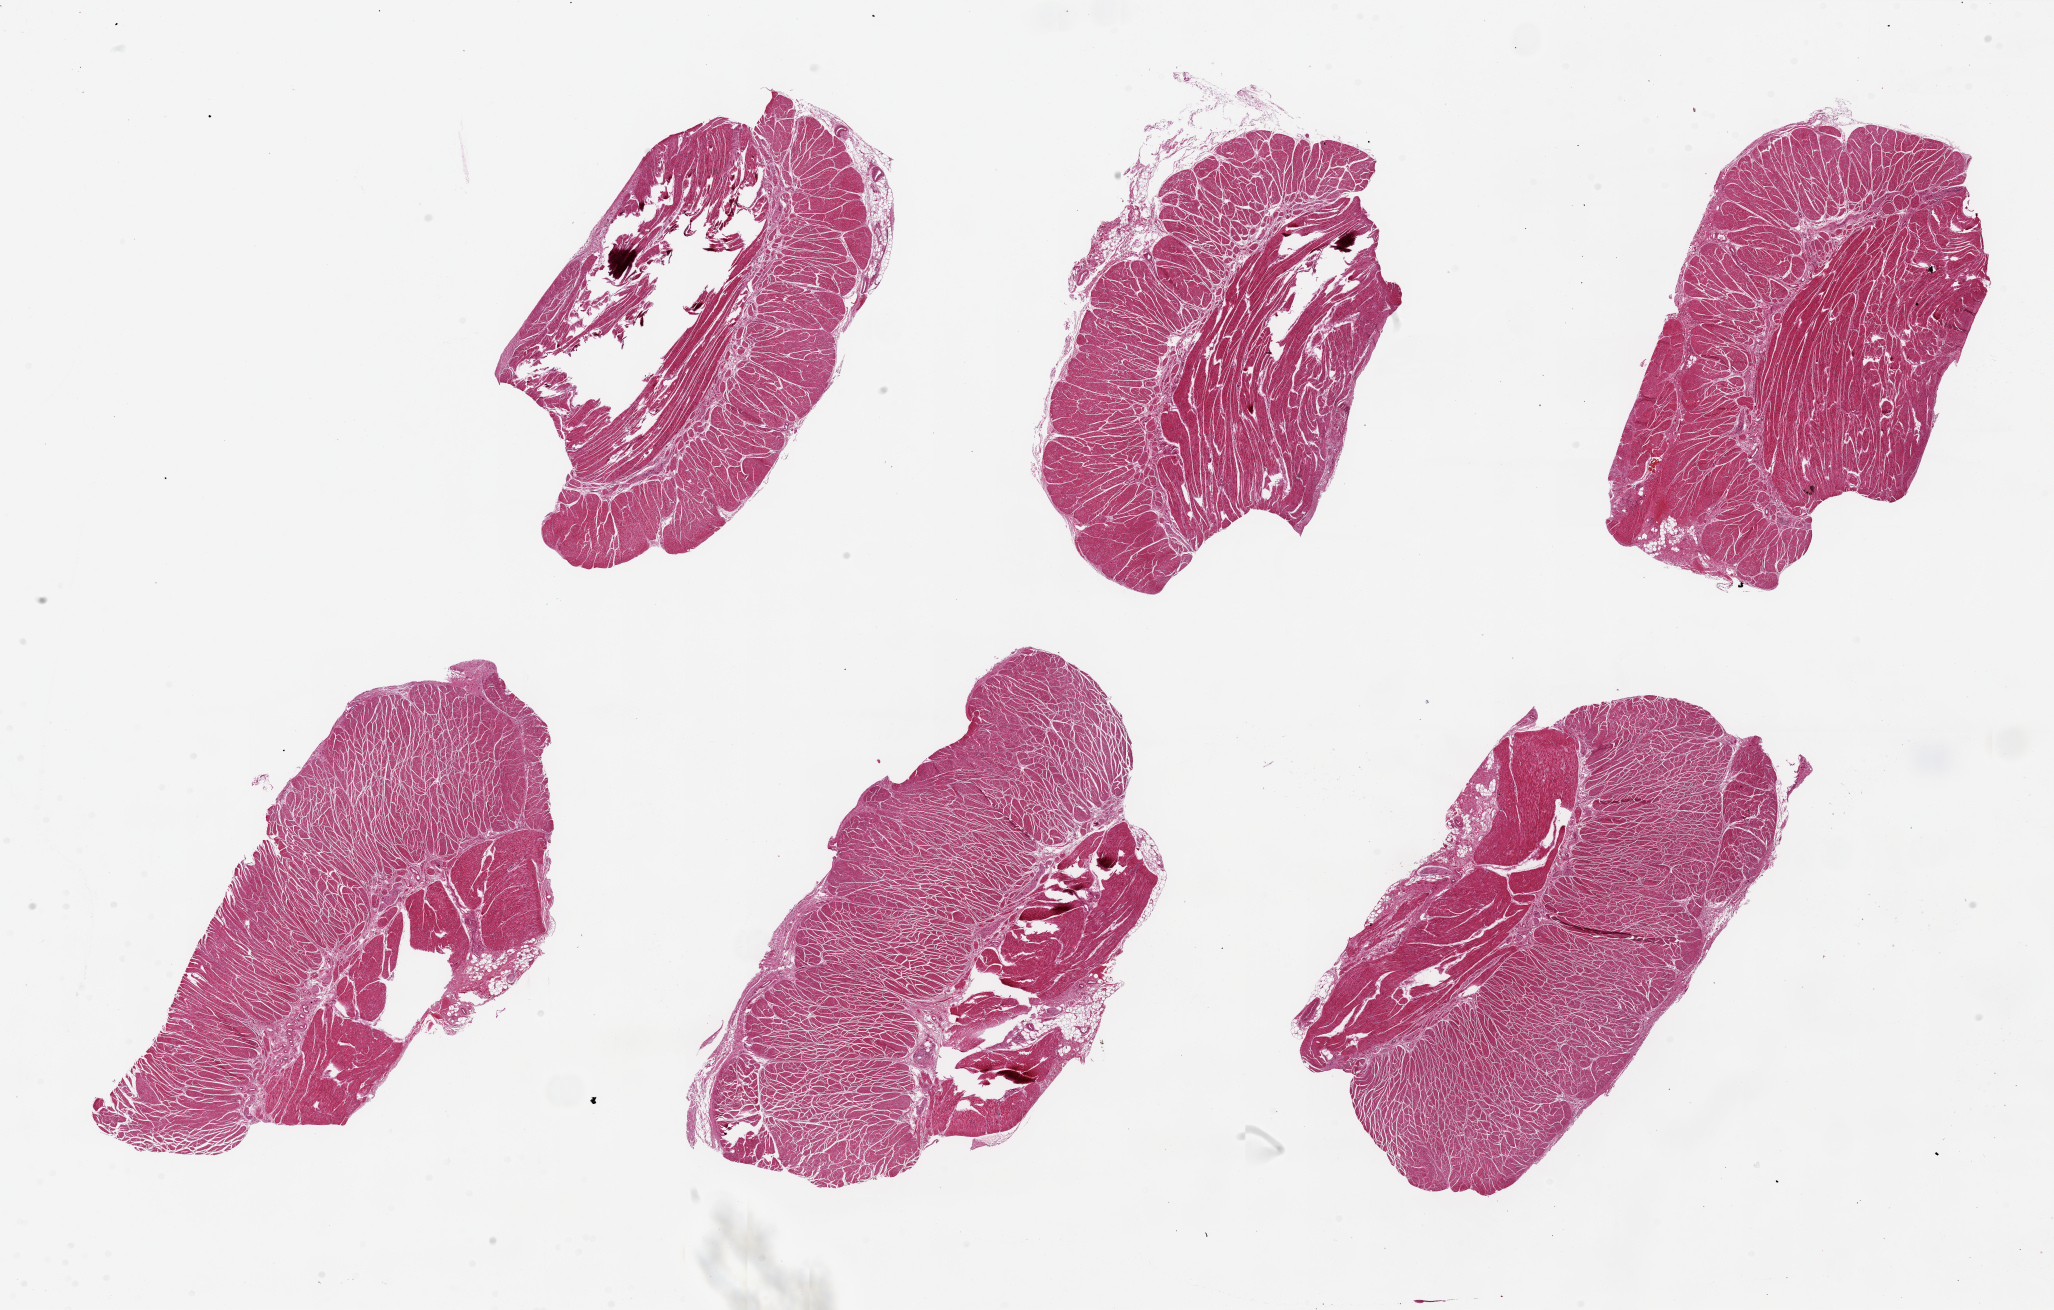
Whole-slide image, haematoxylin and eosin stain, whole scanned area (about 32.5 x 20.7 mm, acquisition: 20x scan) shown as a low-resolution overview; PAXgene-fixed paraffin-embedded (PFPE) section; target tissue: gastroesophageal junction; tissue donor sample. Male donor.
- pathologist's review note for this sample: 6 pieces, up to 9.5x5mm; all muscularis; good specimens